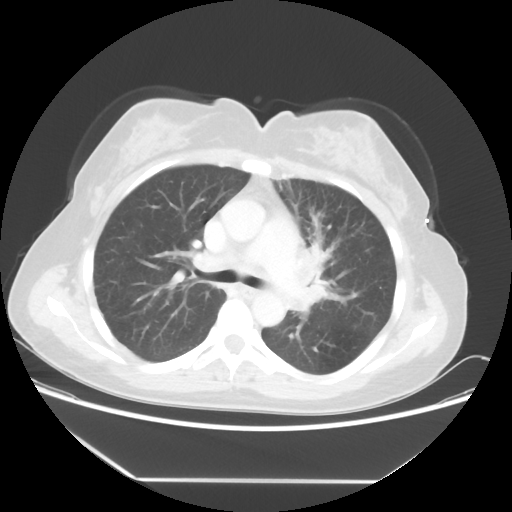
Chest CT, one axial slice; slice 33 of 52 in the series (ordered by position); reconstruction kernel STANDARD; 100 kVp; lung window (W 1500 / L -600 HU); 512 × 512 image matrix, field of view 390 × 390 mm. Patient: female, 50 years. From the clinical record (not read from this slice): clinical TNM (as recorded): T2 N3 M0.
Outlined on this slice (rectangle marked by the reading radiologist):
- lung tumour (recorded histology: adenocarcinoma): box from (x=294, y=237) to (x=343, y=324) px